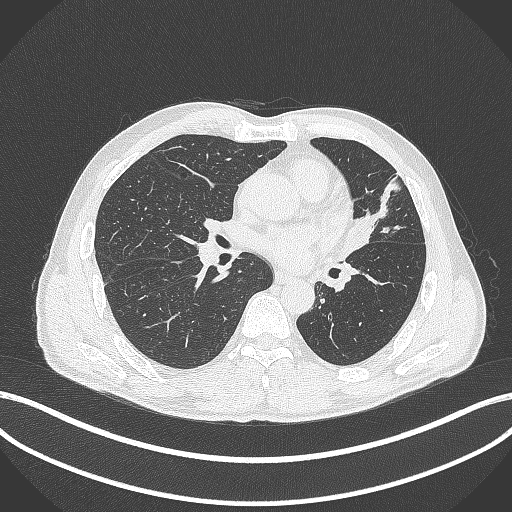
Chest CT, one axial slice. Position 216 of 429 along the scan axis. 120 kVp. Lung window (W 1500 / L -600 HU). 1 mm slice thickness. 512 × 512 image matrix. Male patient, age 57 years. From the clinical record (not read from this slice): clinical TNM (as recorded): T2b N0 M0.
Annotated regions visible in this slice (rectangle marked by the reading radiologist):
- lung tumour (recorded histology: squamous cell carcinoma): bounding box [x1, y1, x2, y2] px = [342, 204, 375, 259]